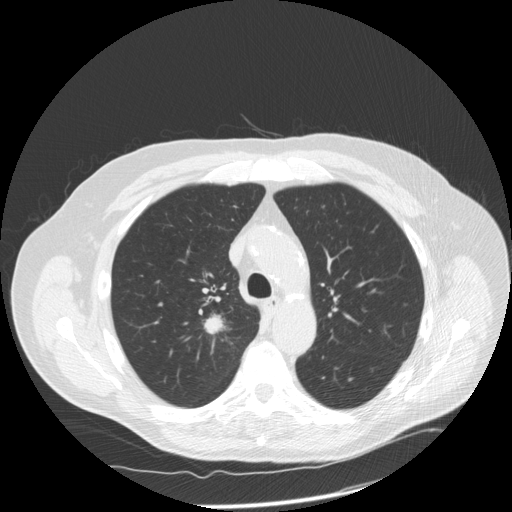
Low-dose screening chest CT, one axial slice; 120 kVp; lung window (W 1500 / L -600 HU); 512 × 512 image matrix, field of view 390 × 390 mm.
Structures marked on this image (outlined manually by an expert reader):
- lesion 1 (tumor, upper lobe of right lung): bounding box (x1, y1, x2, y2) in pixels: (204, 316, 222, 334)